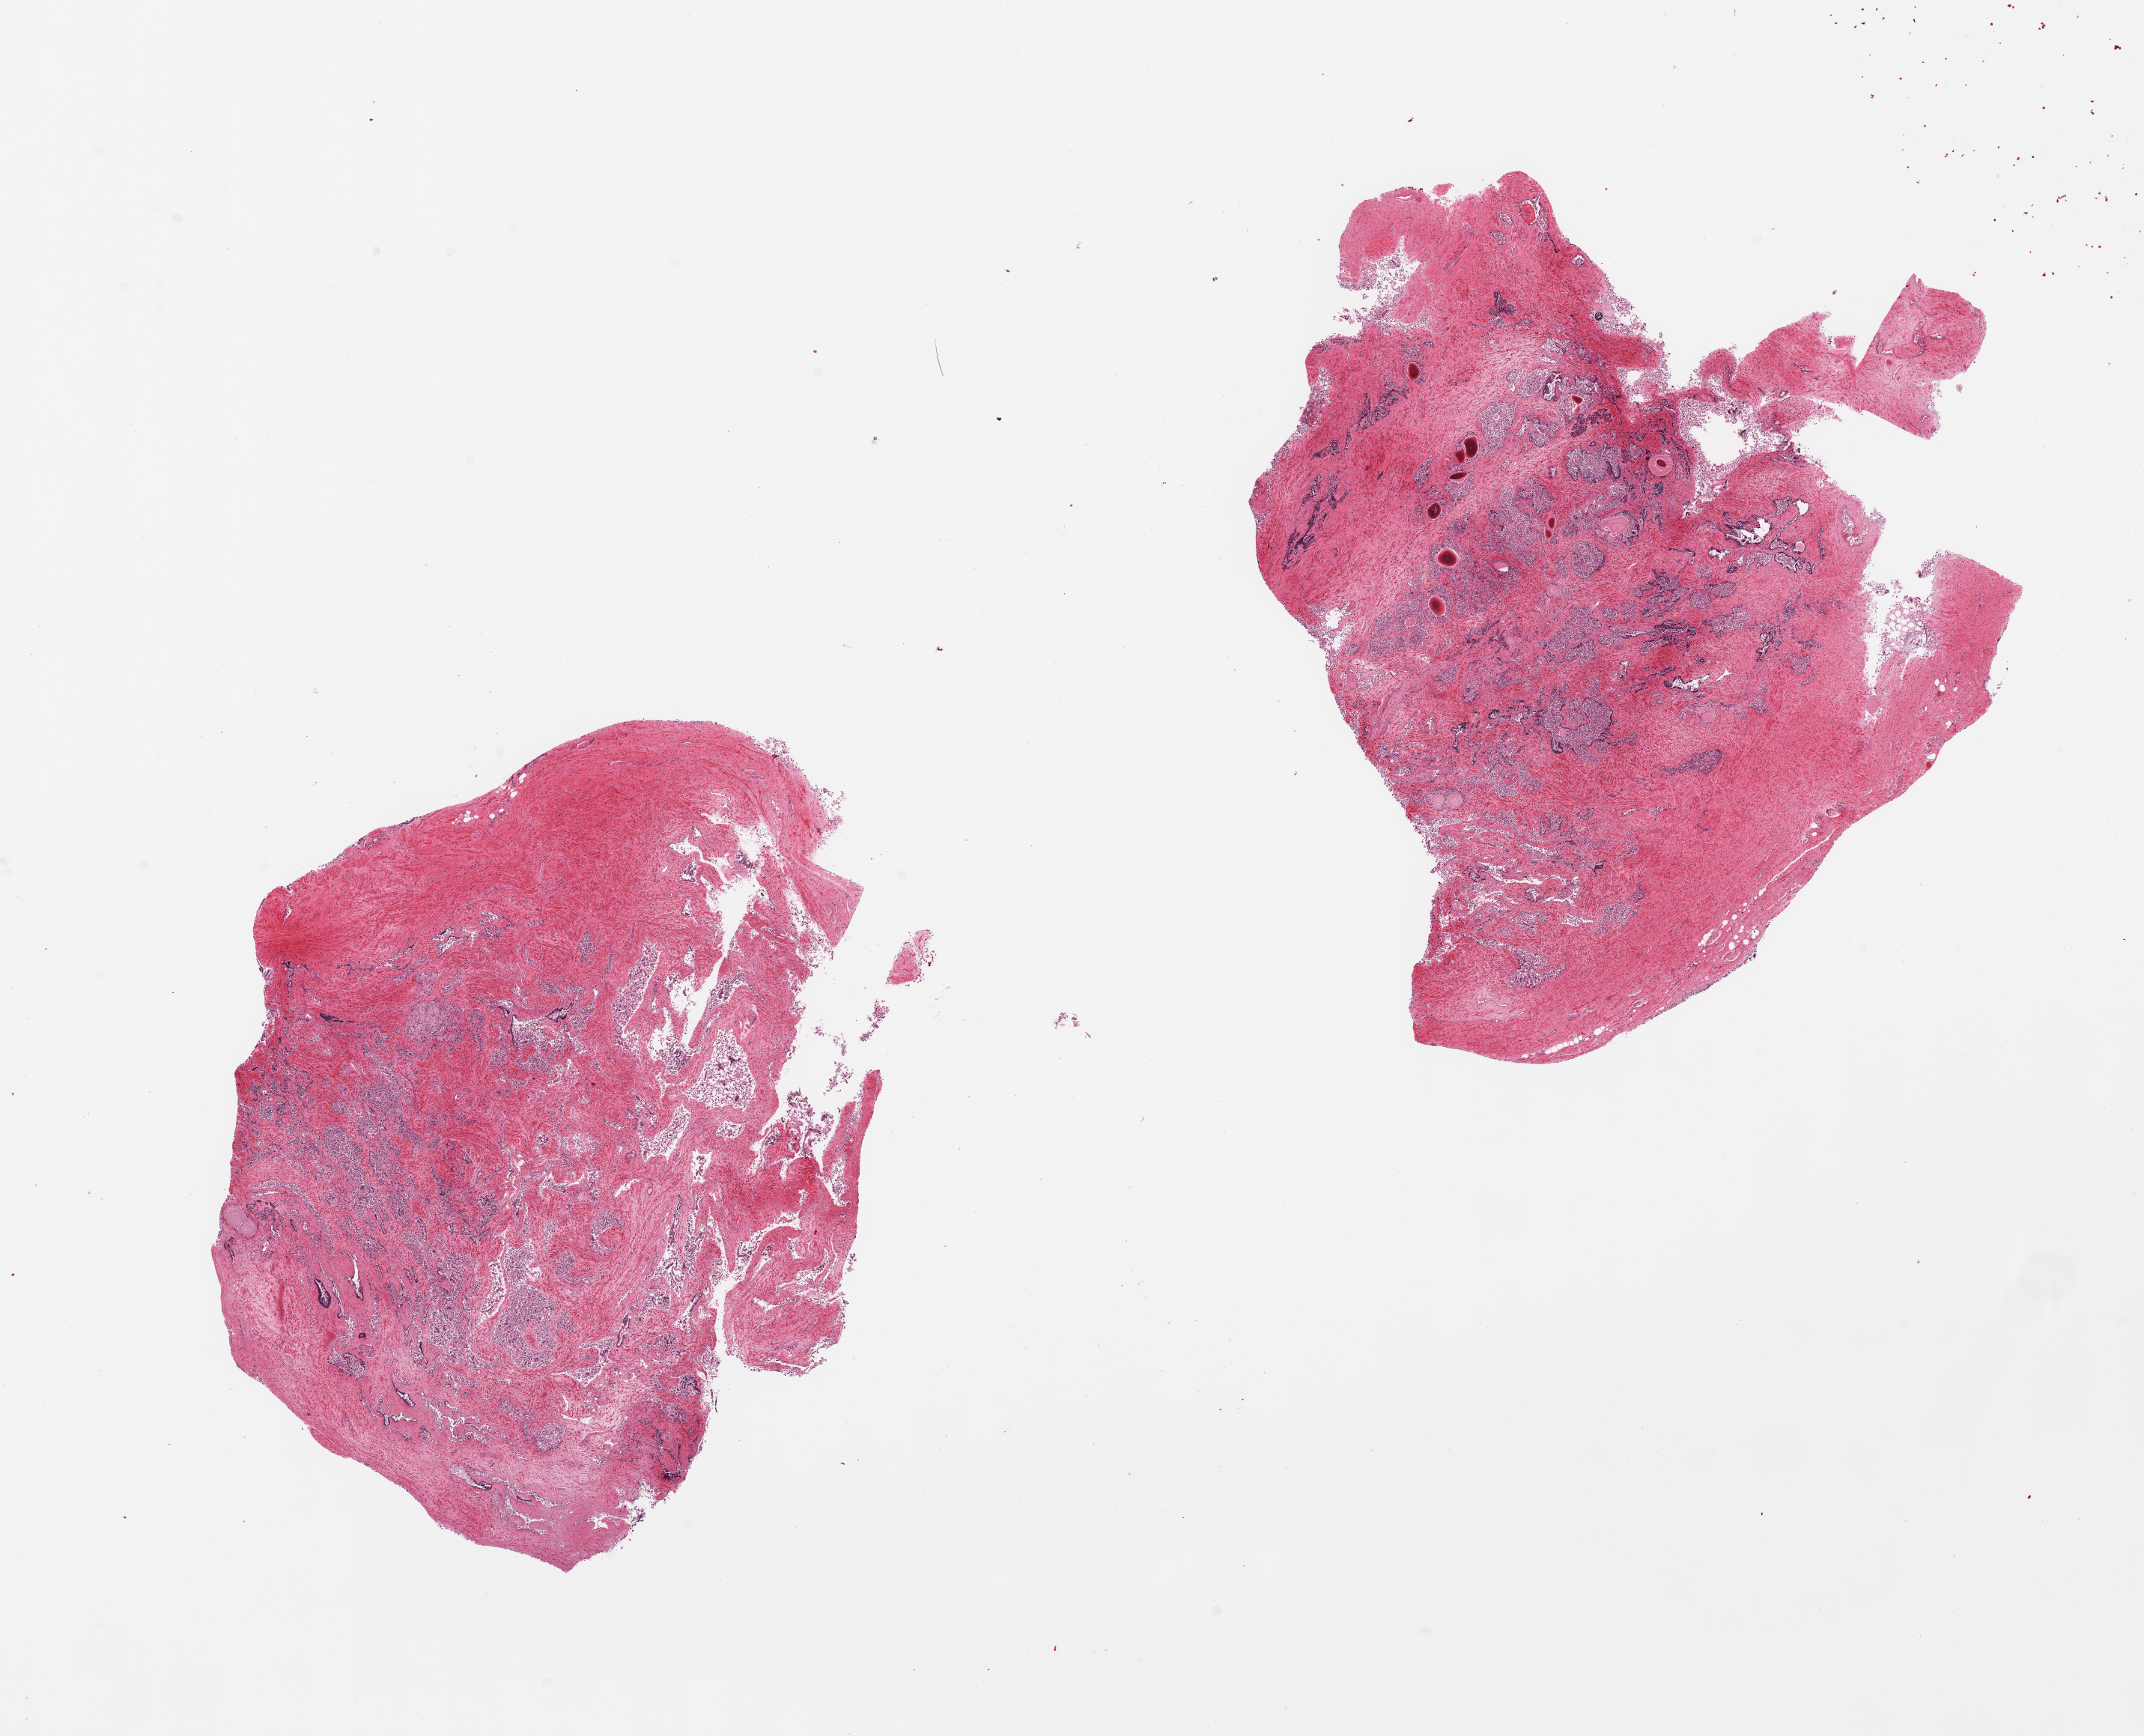
Hematoxylin and eosin (H&E) whole-slide image, brightfield, low-resolution overview of the scanned area, about 22.6 x 18.3 mm (slide scanned at 20x); PAXgene-fixed paraffin-embedded (PFPE) section; section of prostate (target tissue); donor tissue sample. Male donor.
Review note (as recorded): 2 pieces, epithelium almost totally sloughed, corpora amylacea.